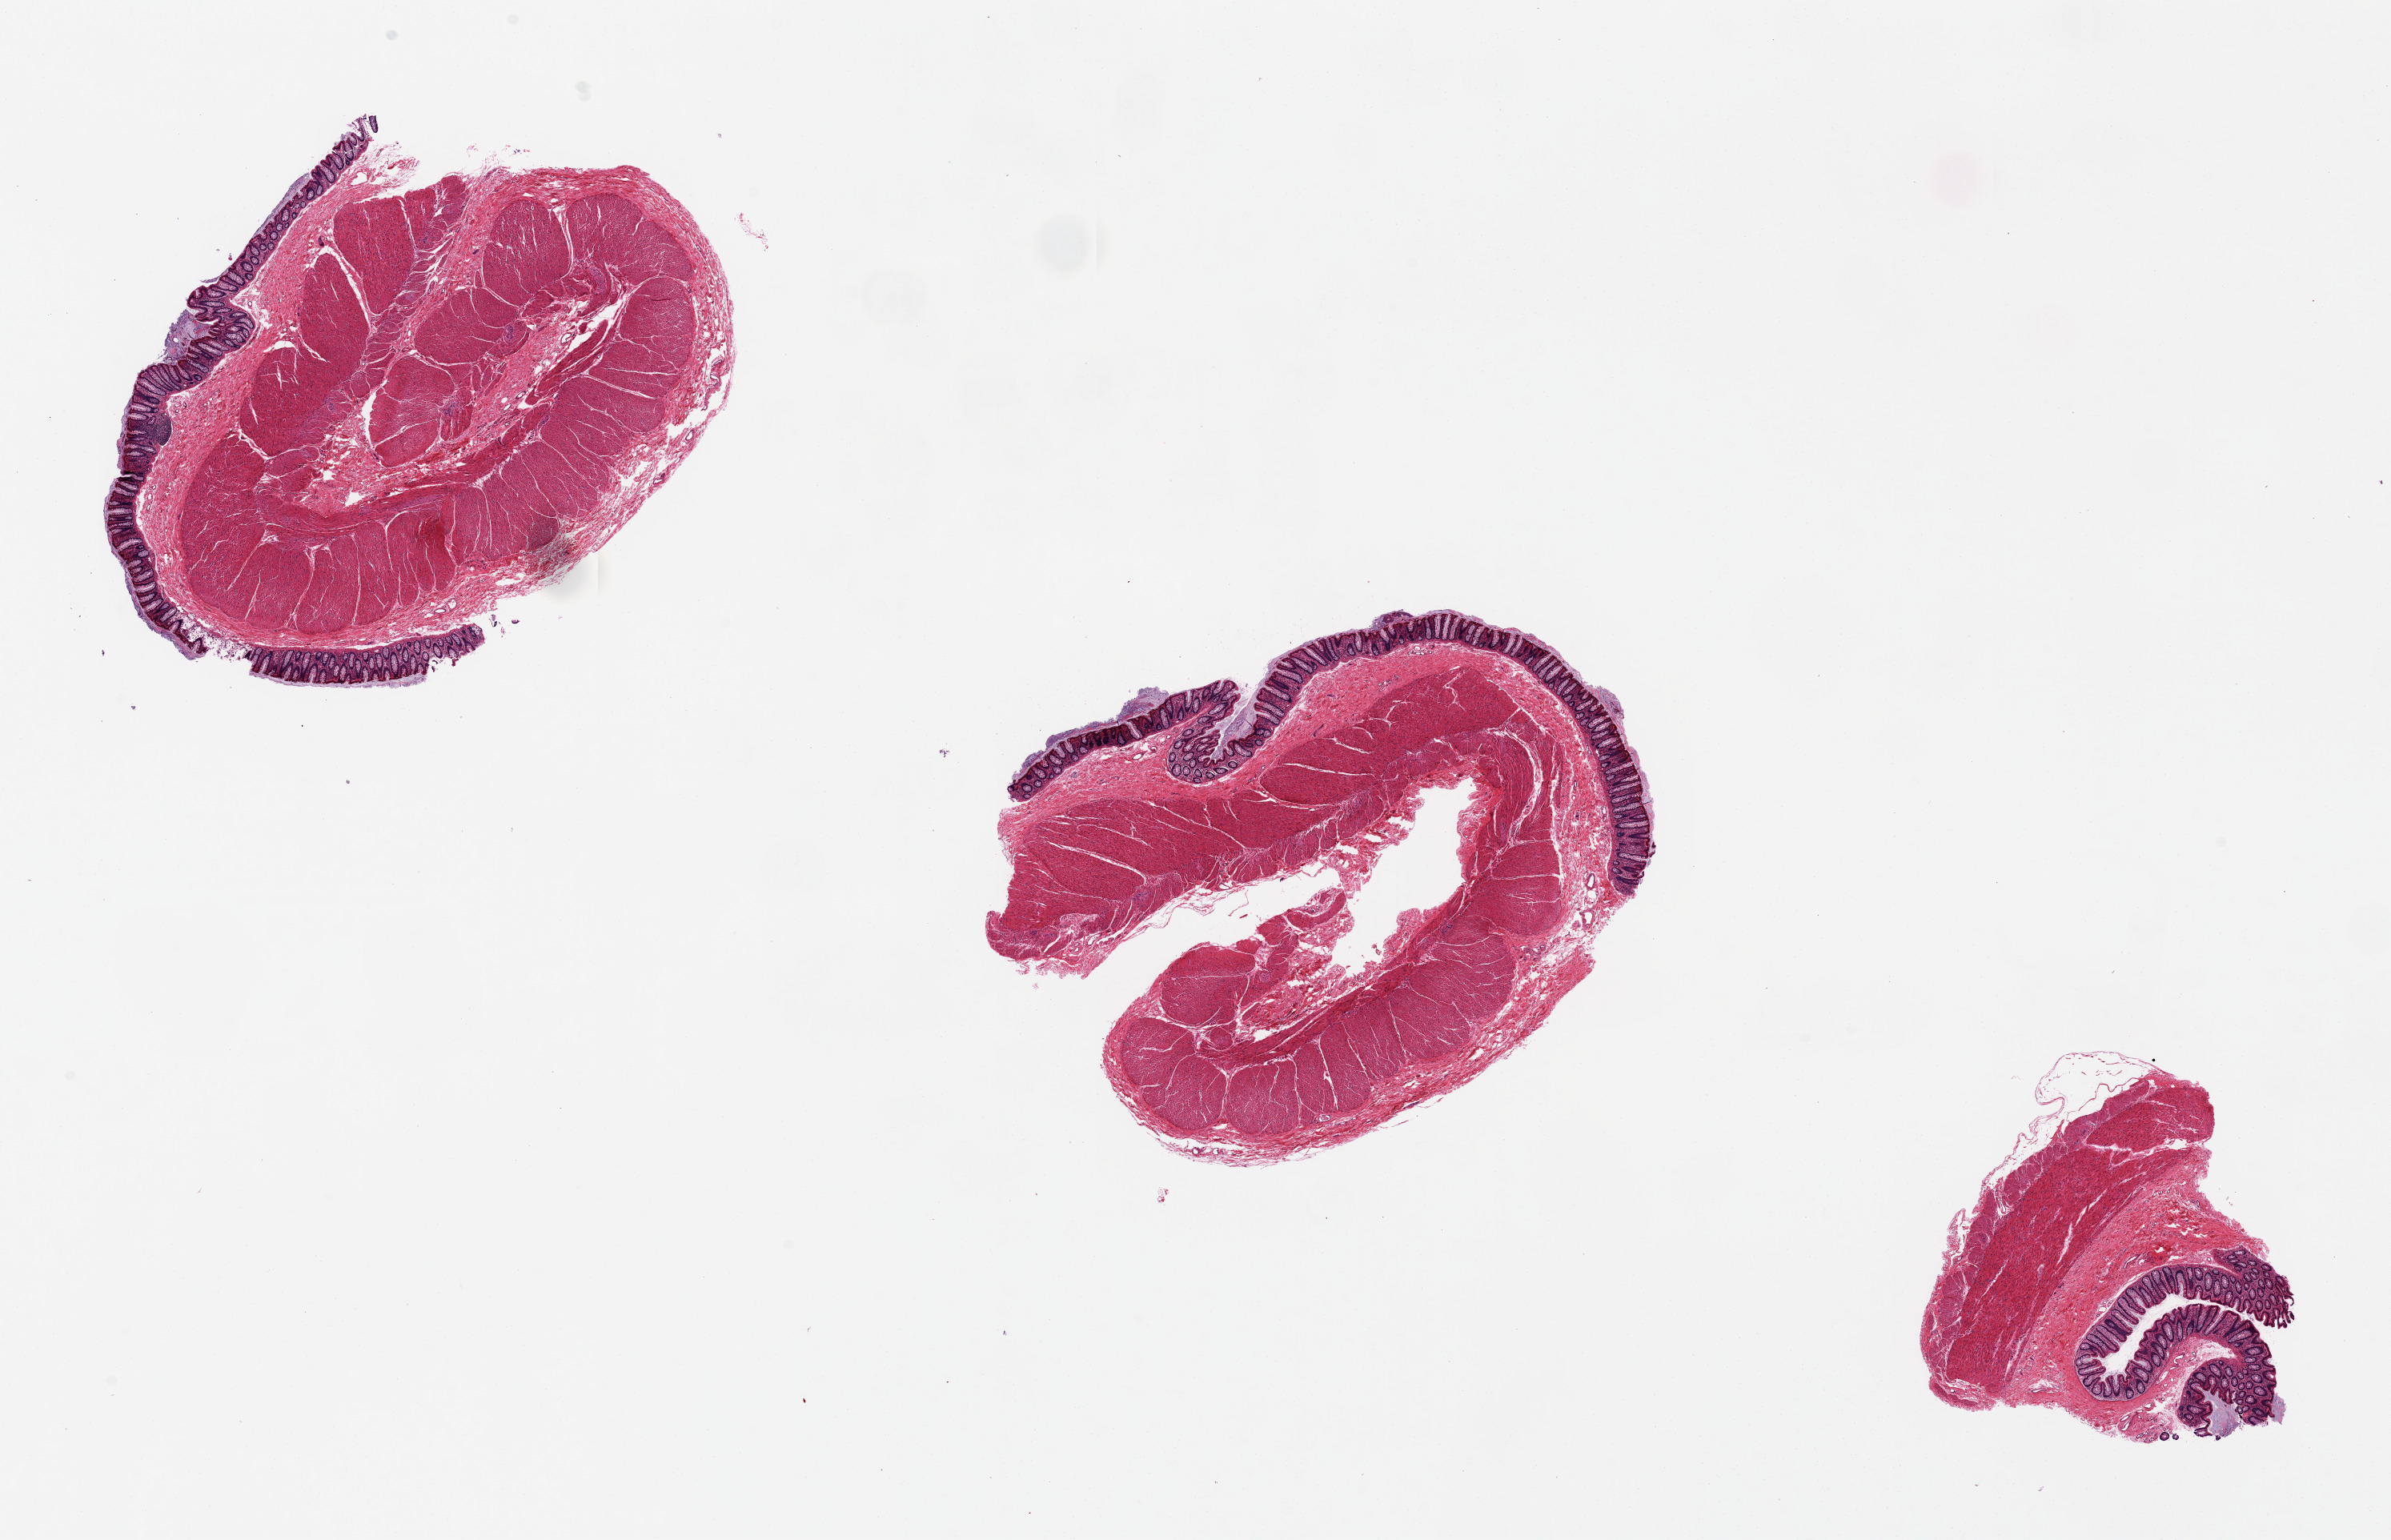
Hematoxylin and eosin (H&E) whole-slide image, brightfield — shown as a low-resolution overview of the whole scanned area (about 23.6 x 15.2 mm); PAXgene-fixed, paraffin-embedded tissue; section of transverse colon (target tissue); donor tissue sample. Male donor.
- review note (as recorded): Remarkably well-preserved epithelium and mucosa. Mucosal thickness ranges from 15-20% of specimen